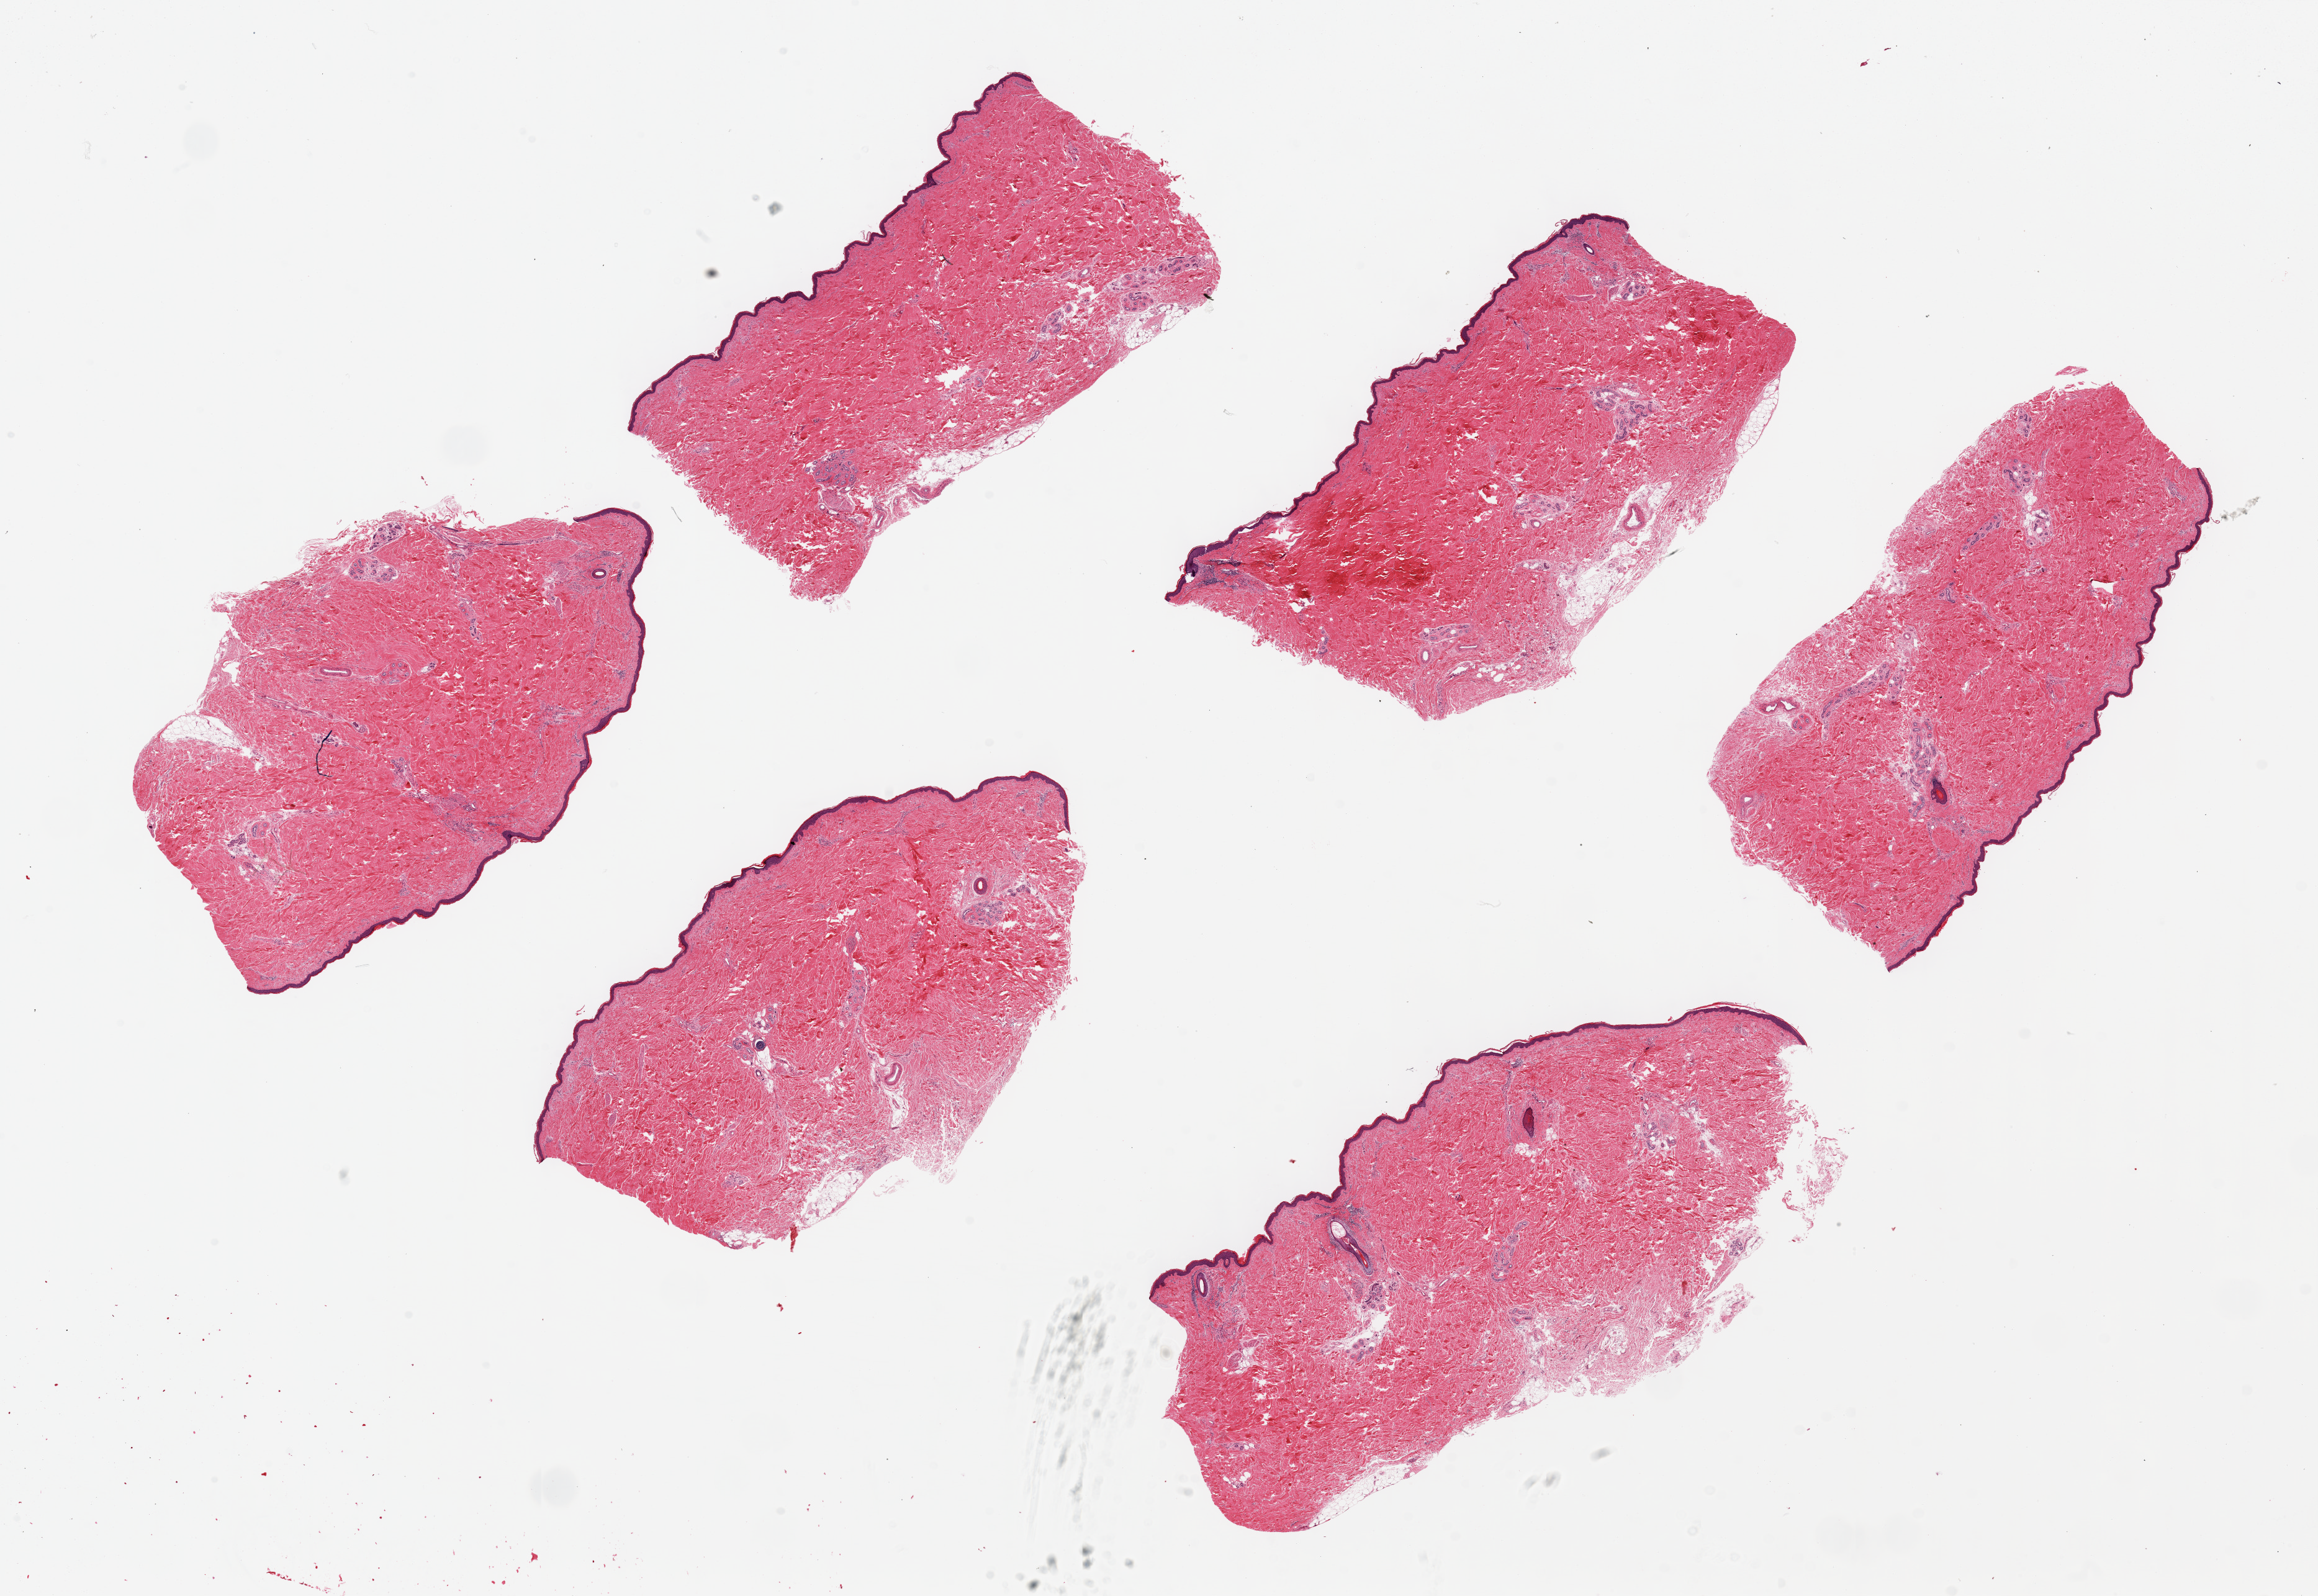
H&E whole-slide image — low-resolution overview of the scanned area, about 29.5 x 20.3 mm, PAXgene-fixed paraffin-embedded (PFPE) section, section of skin of lower leg (target tissue), tissue donor sample. Male donor.
Reviewer comment on this tissue sample: 6 pieces up to 9x4 mm.